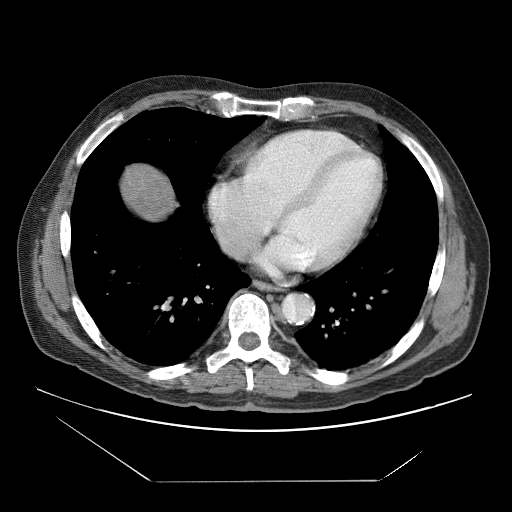
Contrast-enhanced abdominal CT (liver protocol), one axial slice; 120 kVp; soft-tissue window (W 400 / L 40 HU); 512 × 512 image matrix, field of view 420 × 420 mm. From the clinical record (not read from this slice): diagnosis: hepatocellular carcinoma (patient treated with transarterial chemoembolisation; whether this scan precedes or follows treatment is not stated here); TNM stage (as recorded): Stage-IVB; Child-Pugh class: B.
Annotated regions visible in this slice (semi-automatic segmentation, software-assisted and operator-edited):
- abdominal aorta: bounding box <283,294,313,322> (left, top, right, bottom; pixels)
- liver parenchyma outside the tumour (the mass and vessels are separate outlines, so this box may not span the whole liver): <120,164,175,220>